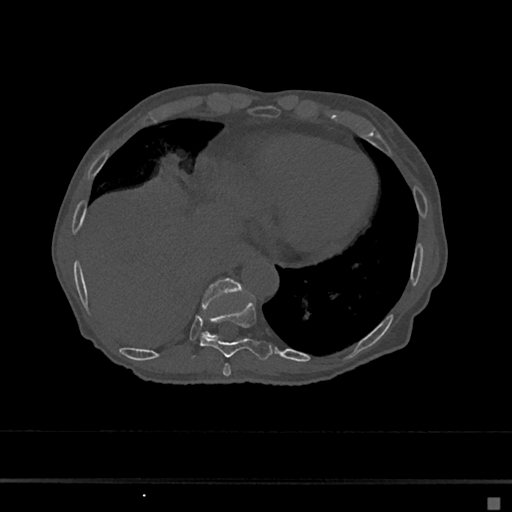
CT including the spine, one axial slice; position 264 of 797 along the scan axis; reconstruction kernel Br40s/3; bone window (W 1800 / L 400 HU); 0.5 mm slice thickness; 512 × 512 image matrix, field of view 360 × 360 mm. Female patient, age 68 years. Case-level facts recorded for this patient, not image findings: primary cancer: renal.
Annotated regions visible in this slice (semi-automatically segmented with operator editing):
- T10 vertebra: bounding box [x1, y1, x2, y2] px = [201, 278, 243, 339]
- T8 vertebra: [223, 363, 231, 376]
- T9 vertebra: [193, 300, 273, 361]